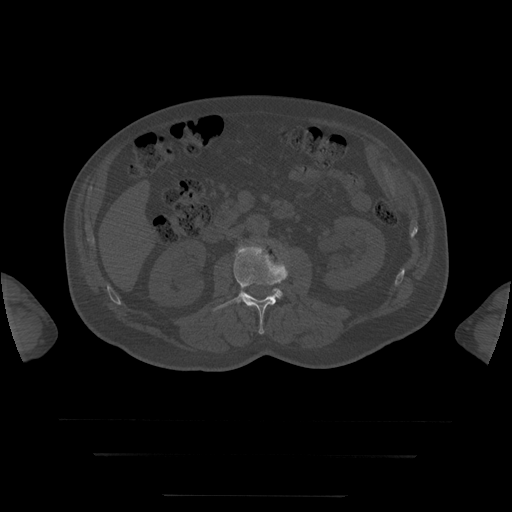
CT including the spine, one axial slice; position 18 of 397 along the scan axis; reconstruction kernel STANDARD; 120 kVp; bone window (W 1800 / L 400 HU); 1.25 mm slice thickness; 512 × 512 image matrix. Patient age 73 years. From the clinical record (not read from this slice): primary cancer: prostate.
Outlined on this slice (semi-automatic segmentation, software-assisted and operator-edited):
- L3 vertebra: bounding box (x1, y1, x2, y2) in pixels: (276, 266, 289, 298)